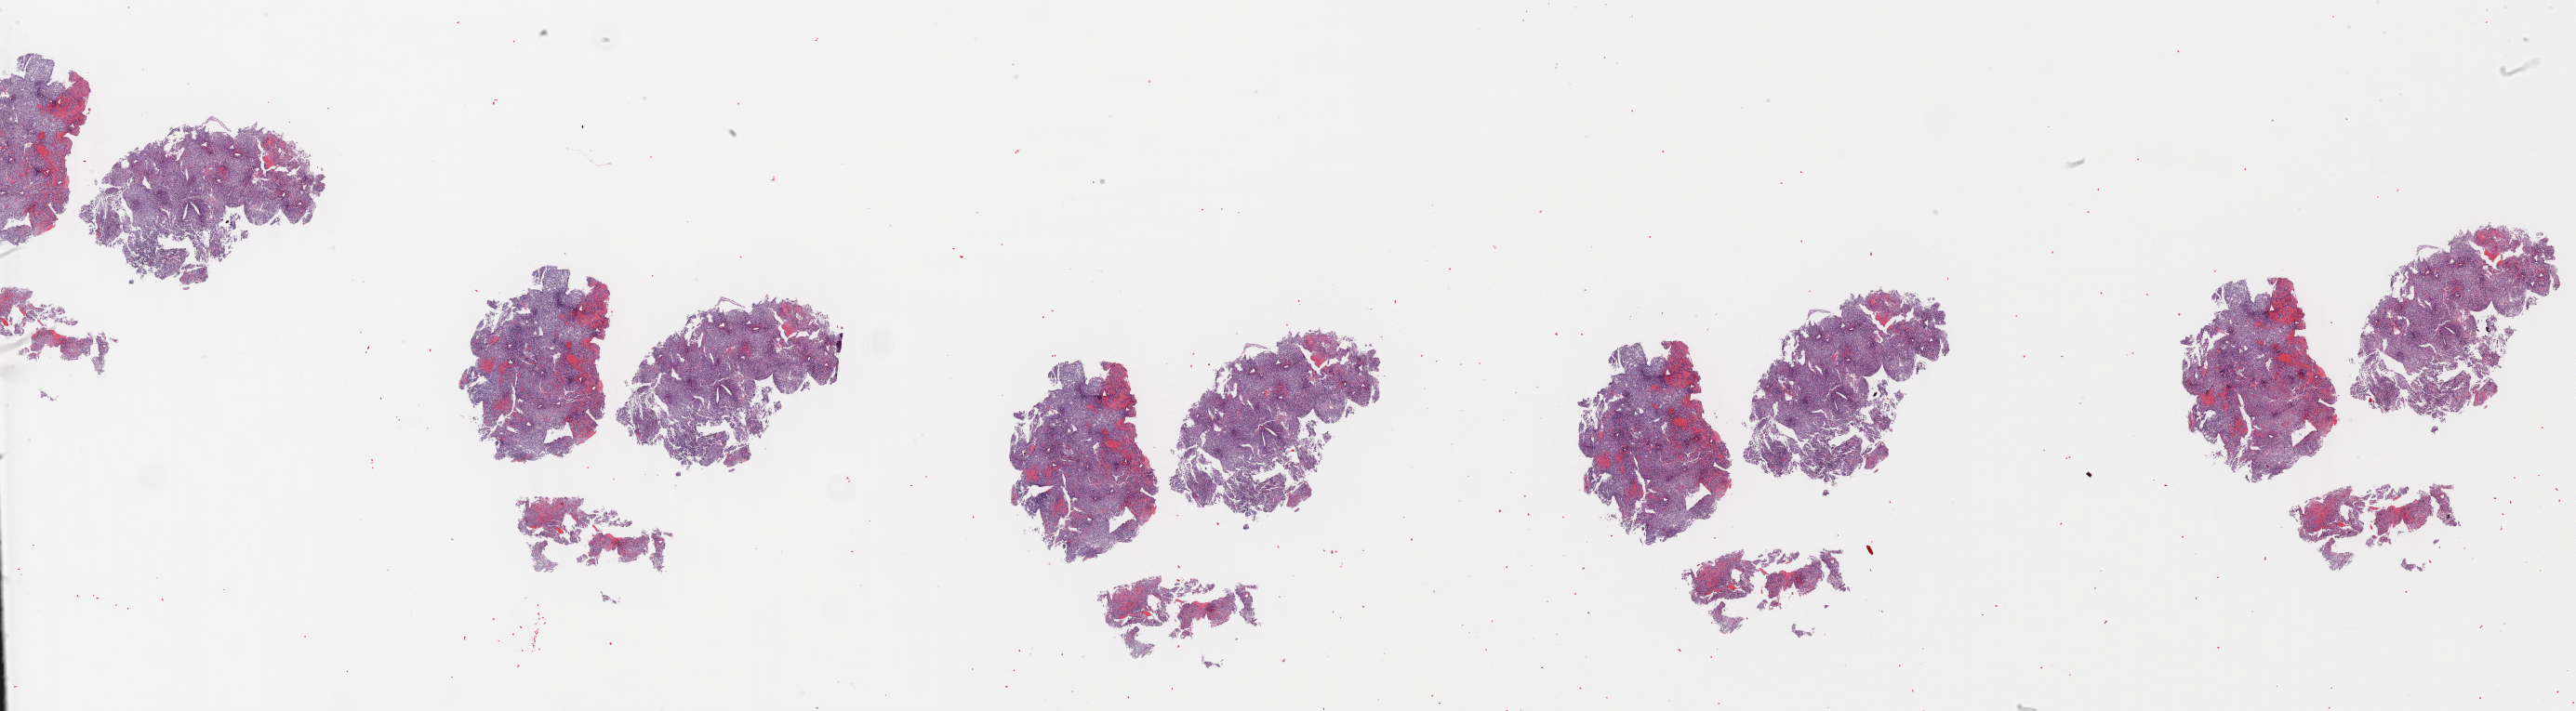
H&E whole-slide image — a low-resolution overview of the entire scanned area, about 44.8 x 12.4 mm (acquisition: 40x scan), formalin-fixed paraffin-embedded (FFPE) diagnostic section, brain, primary tumour sample. Patient: male, age at initial diagnosis 62 years.
Pathologic diagnosis: Oligodendroglioma, NOS (cerebrum).